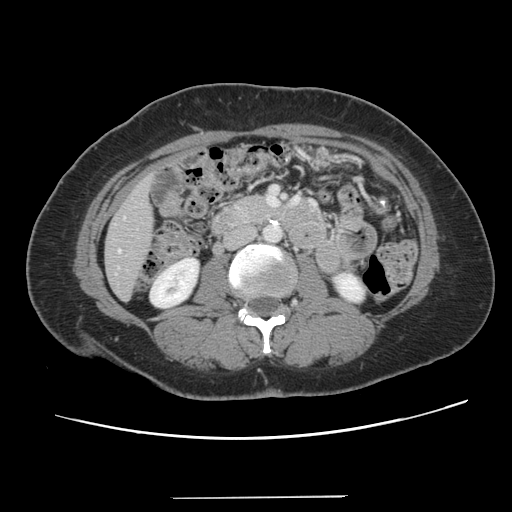
Contrast-enhanced abdominal CT, one axial slice; position 35 of 141 along the scan axis; intravenous contrast given; soft-tissue window (W 400 / L 40 HU); 2.5 mm slice thickness; 512 × 512 image matrix, field of view 366 × 366 mm. Female patient, age 53 years. From the clinical record (not read from this slice): diagnosis: colorectal cancer liver metastases, imaged before liver resection; multiple liver metastases: no; largest metastasis: 14.5 cm; chemotherapy before resection: yes.
Outlined on this slice (manually delineated by an expert):
- liver: bounding box [x1, y1, x2, y2] px = [106, 179, 155, 300]
- planned liver remnant (the part of the liver to remain after resection): [105, 211, 154, 299]